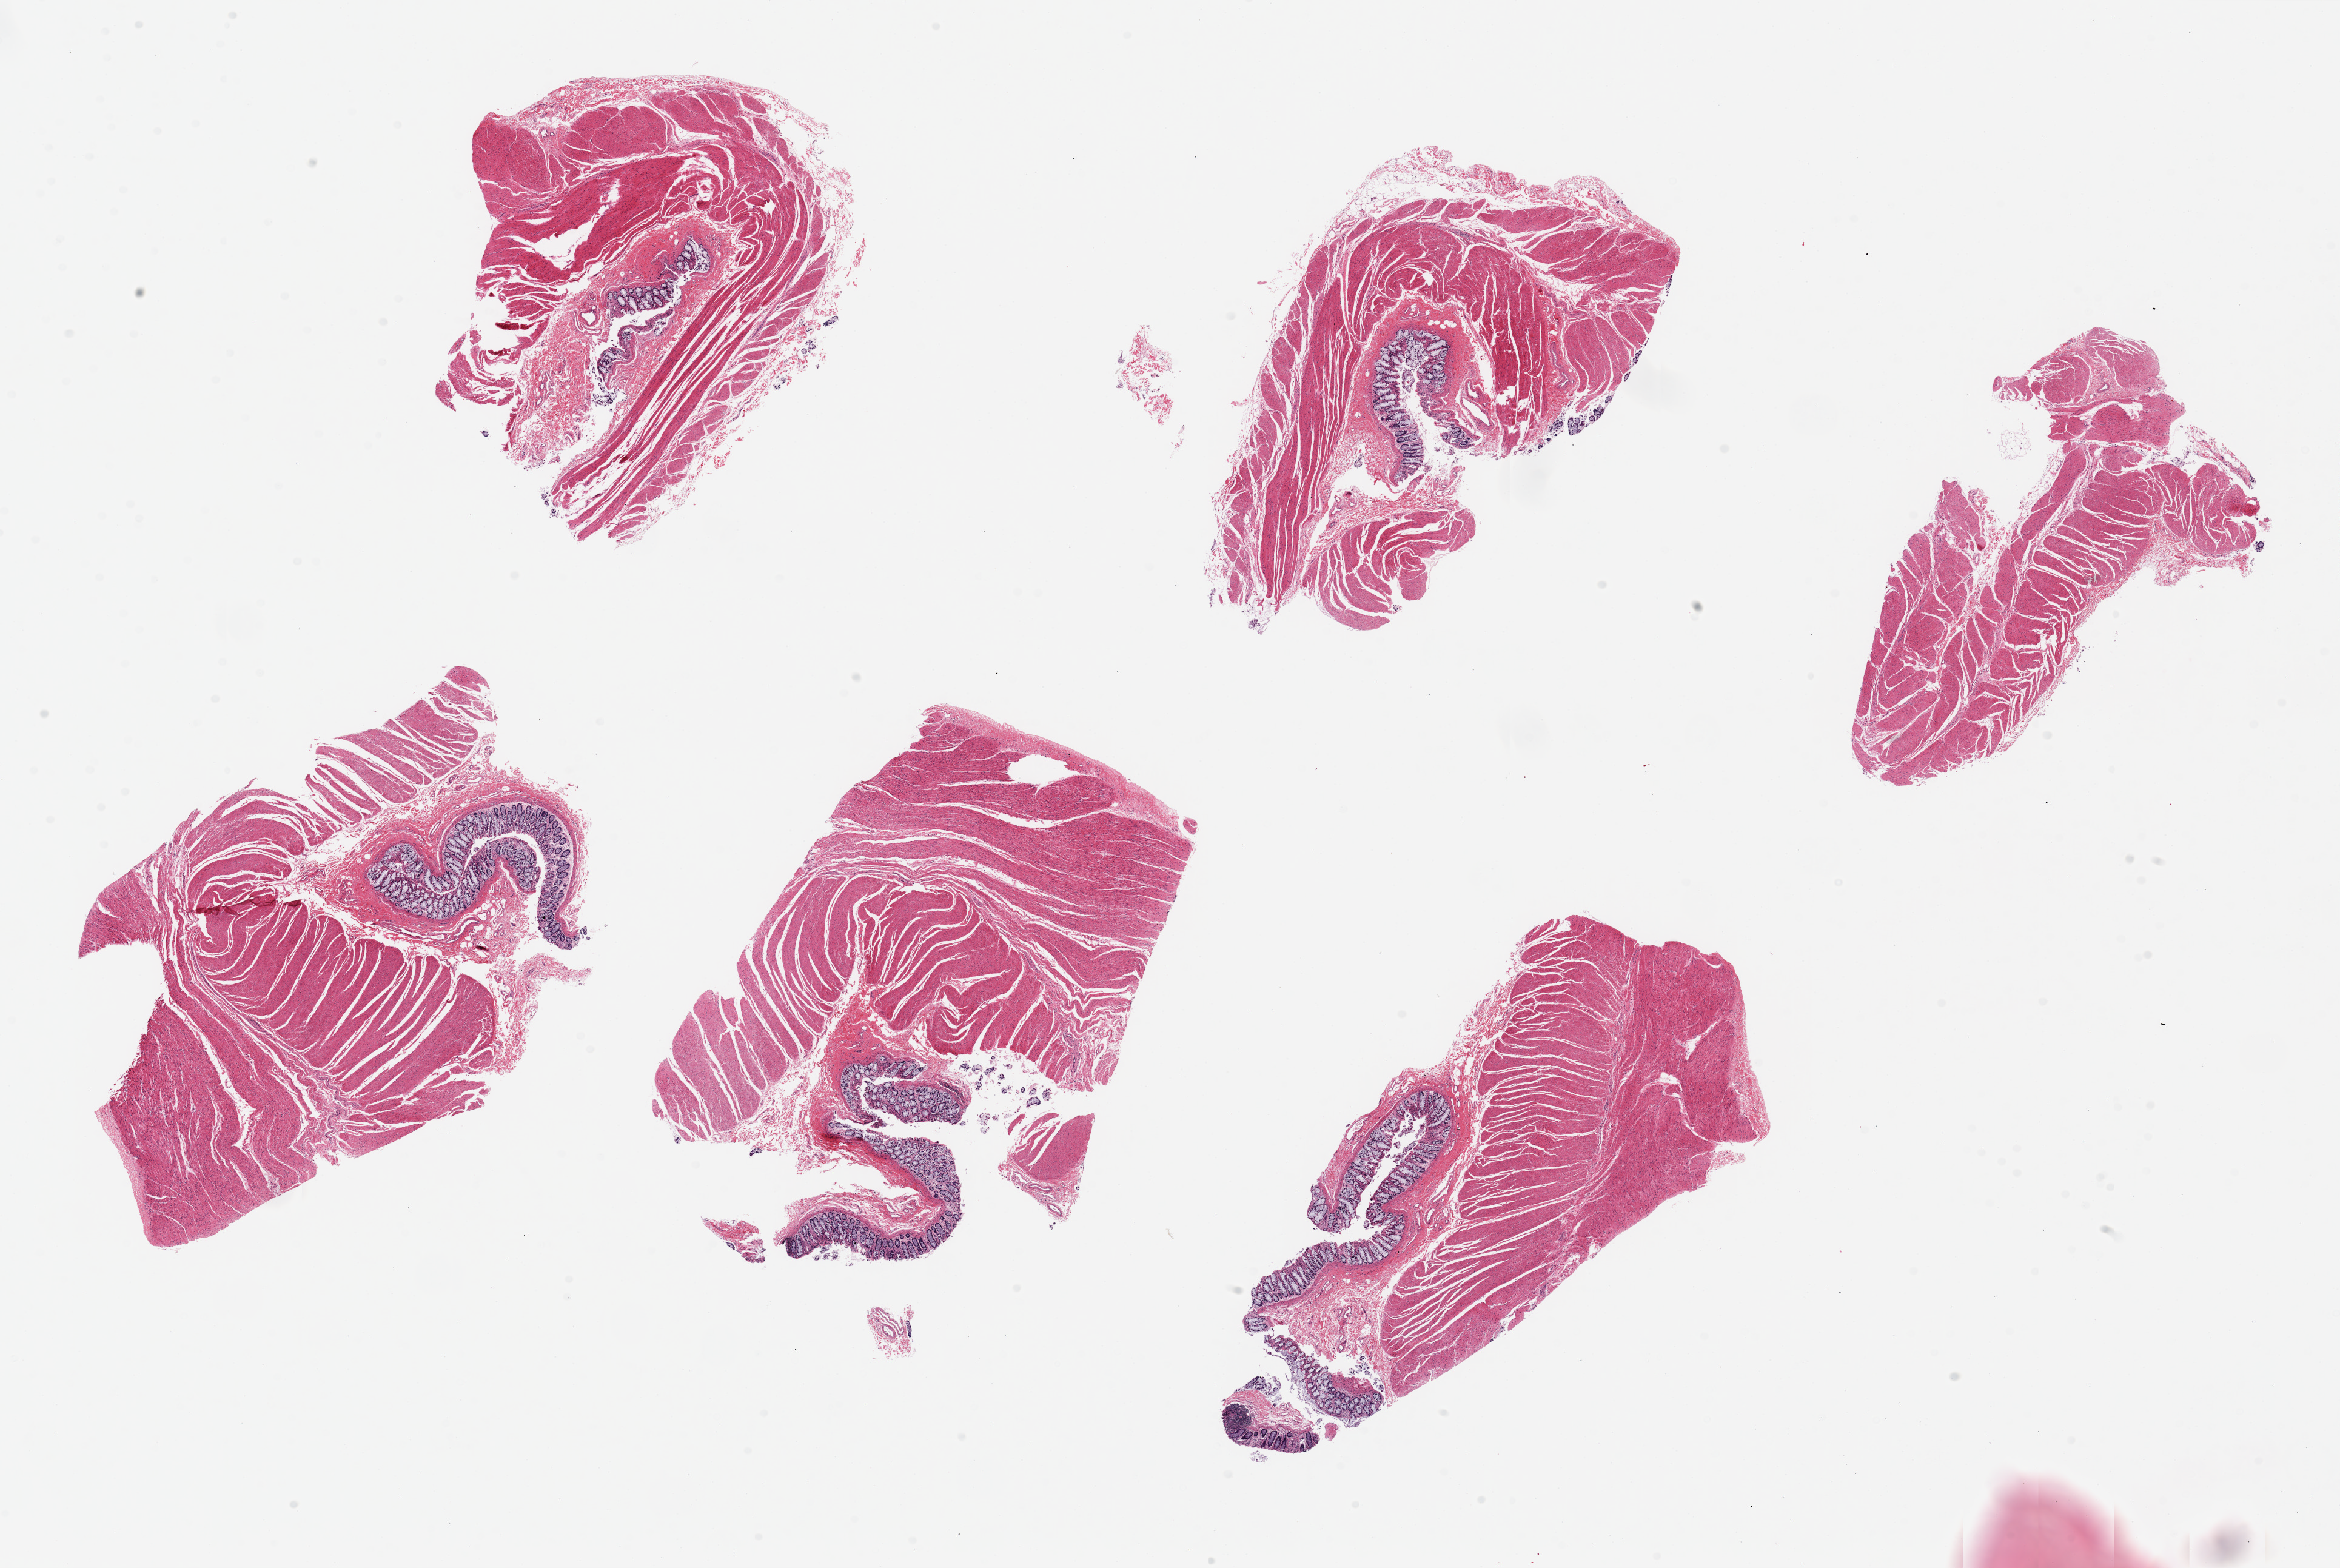
Hematoxylin and eosin (H&E) whole-slide image — whole scanned area (about 30.5 x 20.5 mm) shown as a low-resolution overview. PAXgene-fixed paraffin-embedded (PFPE) section. Target tissue: sigmoid colon. Tissue donor sample. Donor: female.
- pathologist's review note for this sample: 6 pieces ~7x4mm, mainly muscularis, ~10 mucosa present, moderately preserved